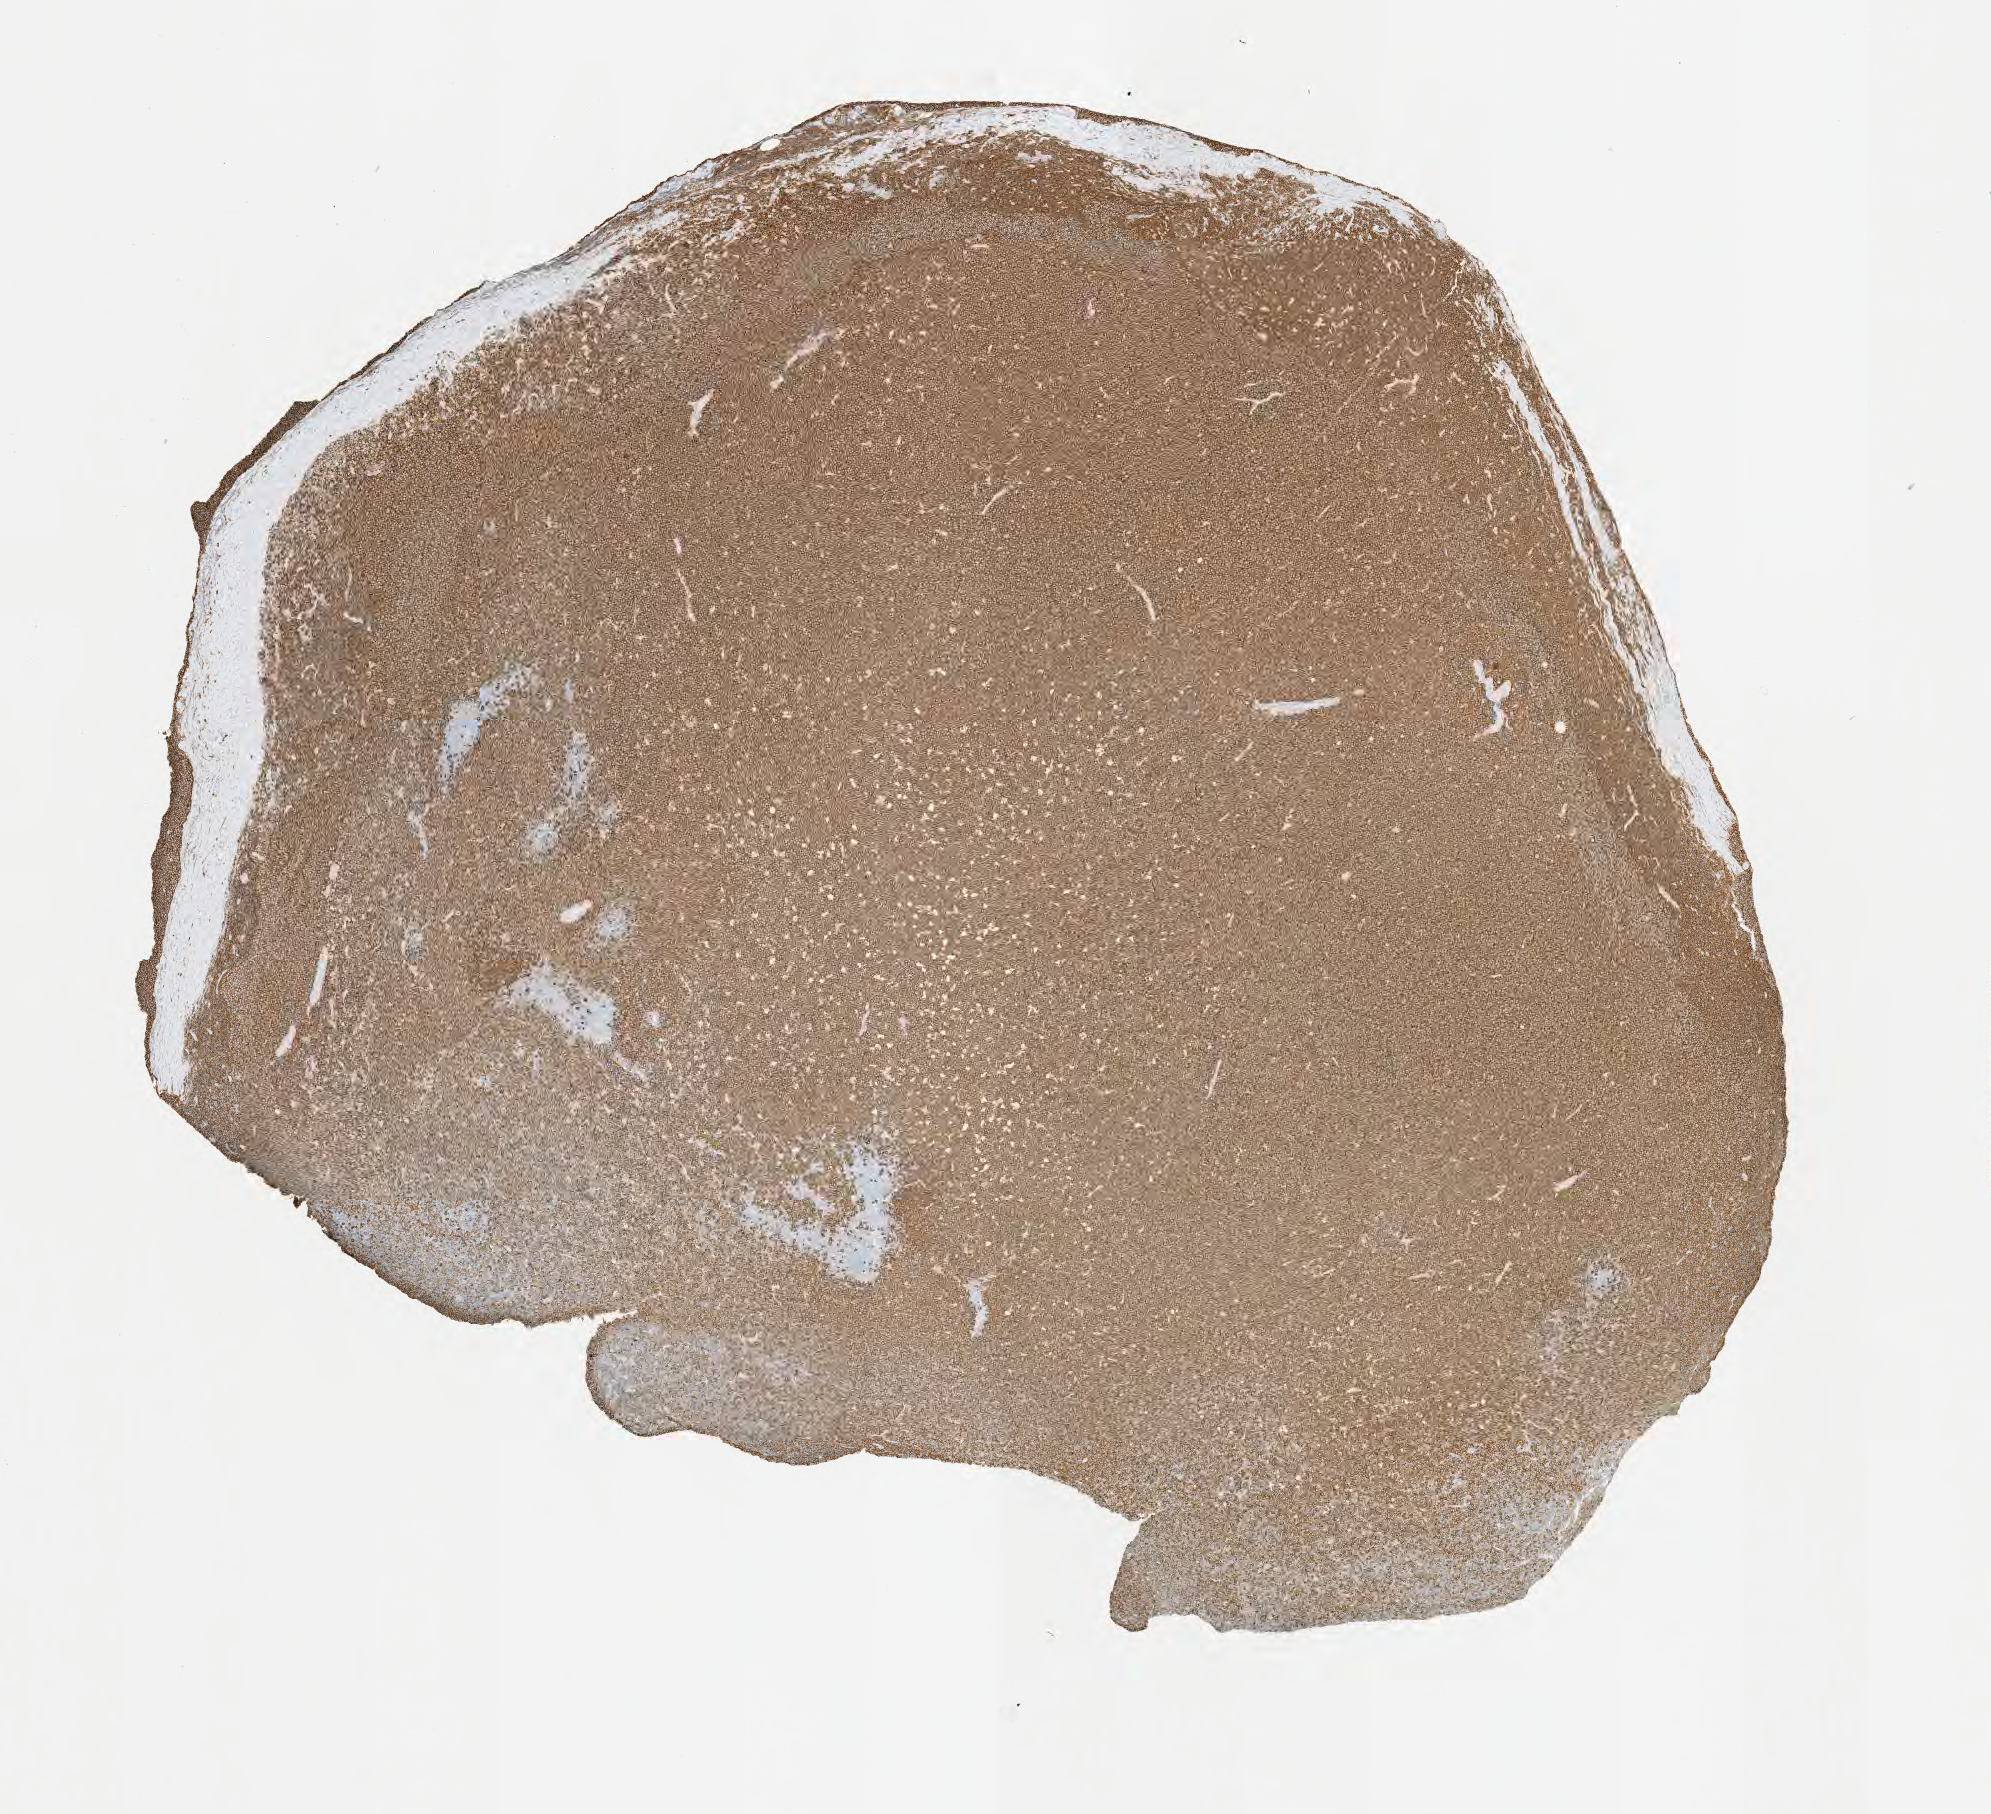
IHC for CD20, whole-slide image, a low-resolution overview of the entire scanned area, about 8.1 x 7.3 mm; specimen: tumor tissue. Patient: male, aged 45.
Histologic diagnosis: Burkitt lymphoma, NOS.